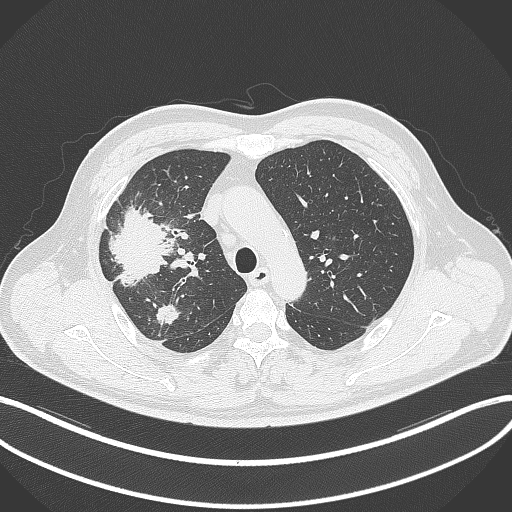
Chest CT, one axial slice; position 244 of 348 along the scan axis; 120 kVp; lung window (W 1500 / L -600 HU); 1 mm slice thickness; 512 × 512 image matrix, field of view 400 × 400 mm. Patient: male, 55 years. Case-level facts recorded for this patient, not image findings: clinical TNM (as recorded): T3 N2 M1.
Annotated regions visible in this slice (bounding box drawn by a radiologist):
- lung tumour (recorded histology: adenocarcinoma): bounding box (x1, y1, x2, y2) in pixels: (105, 201, 177, 286)